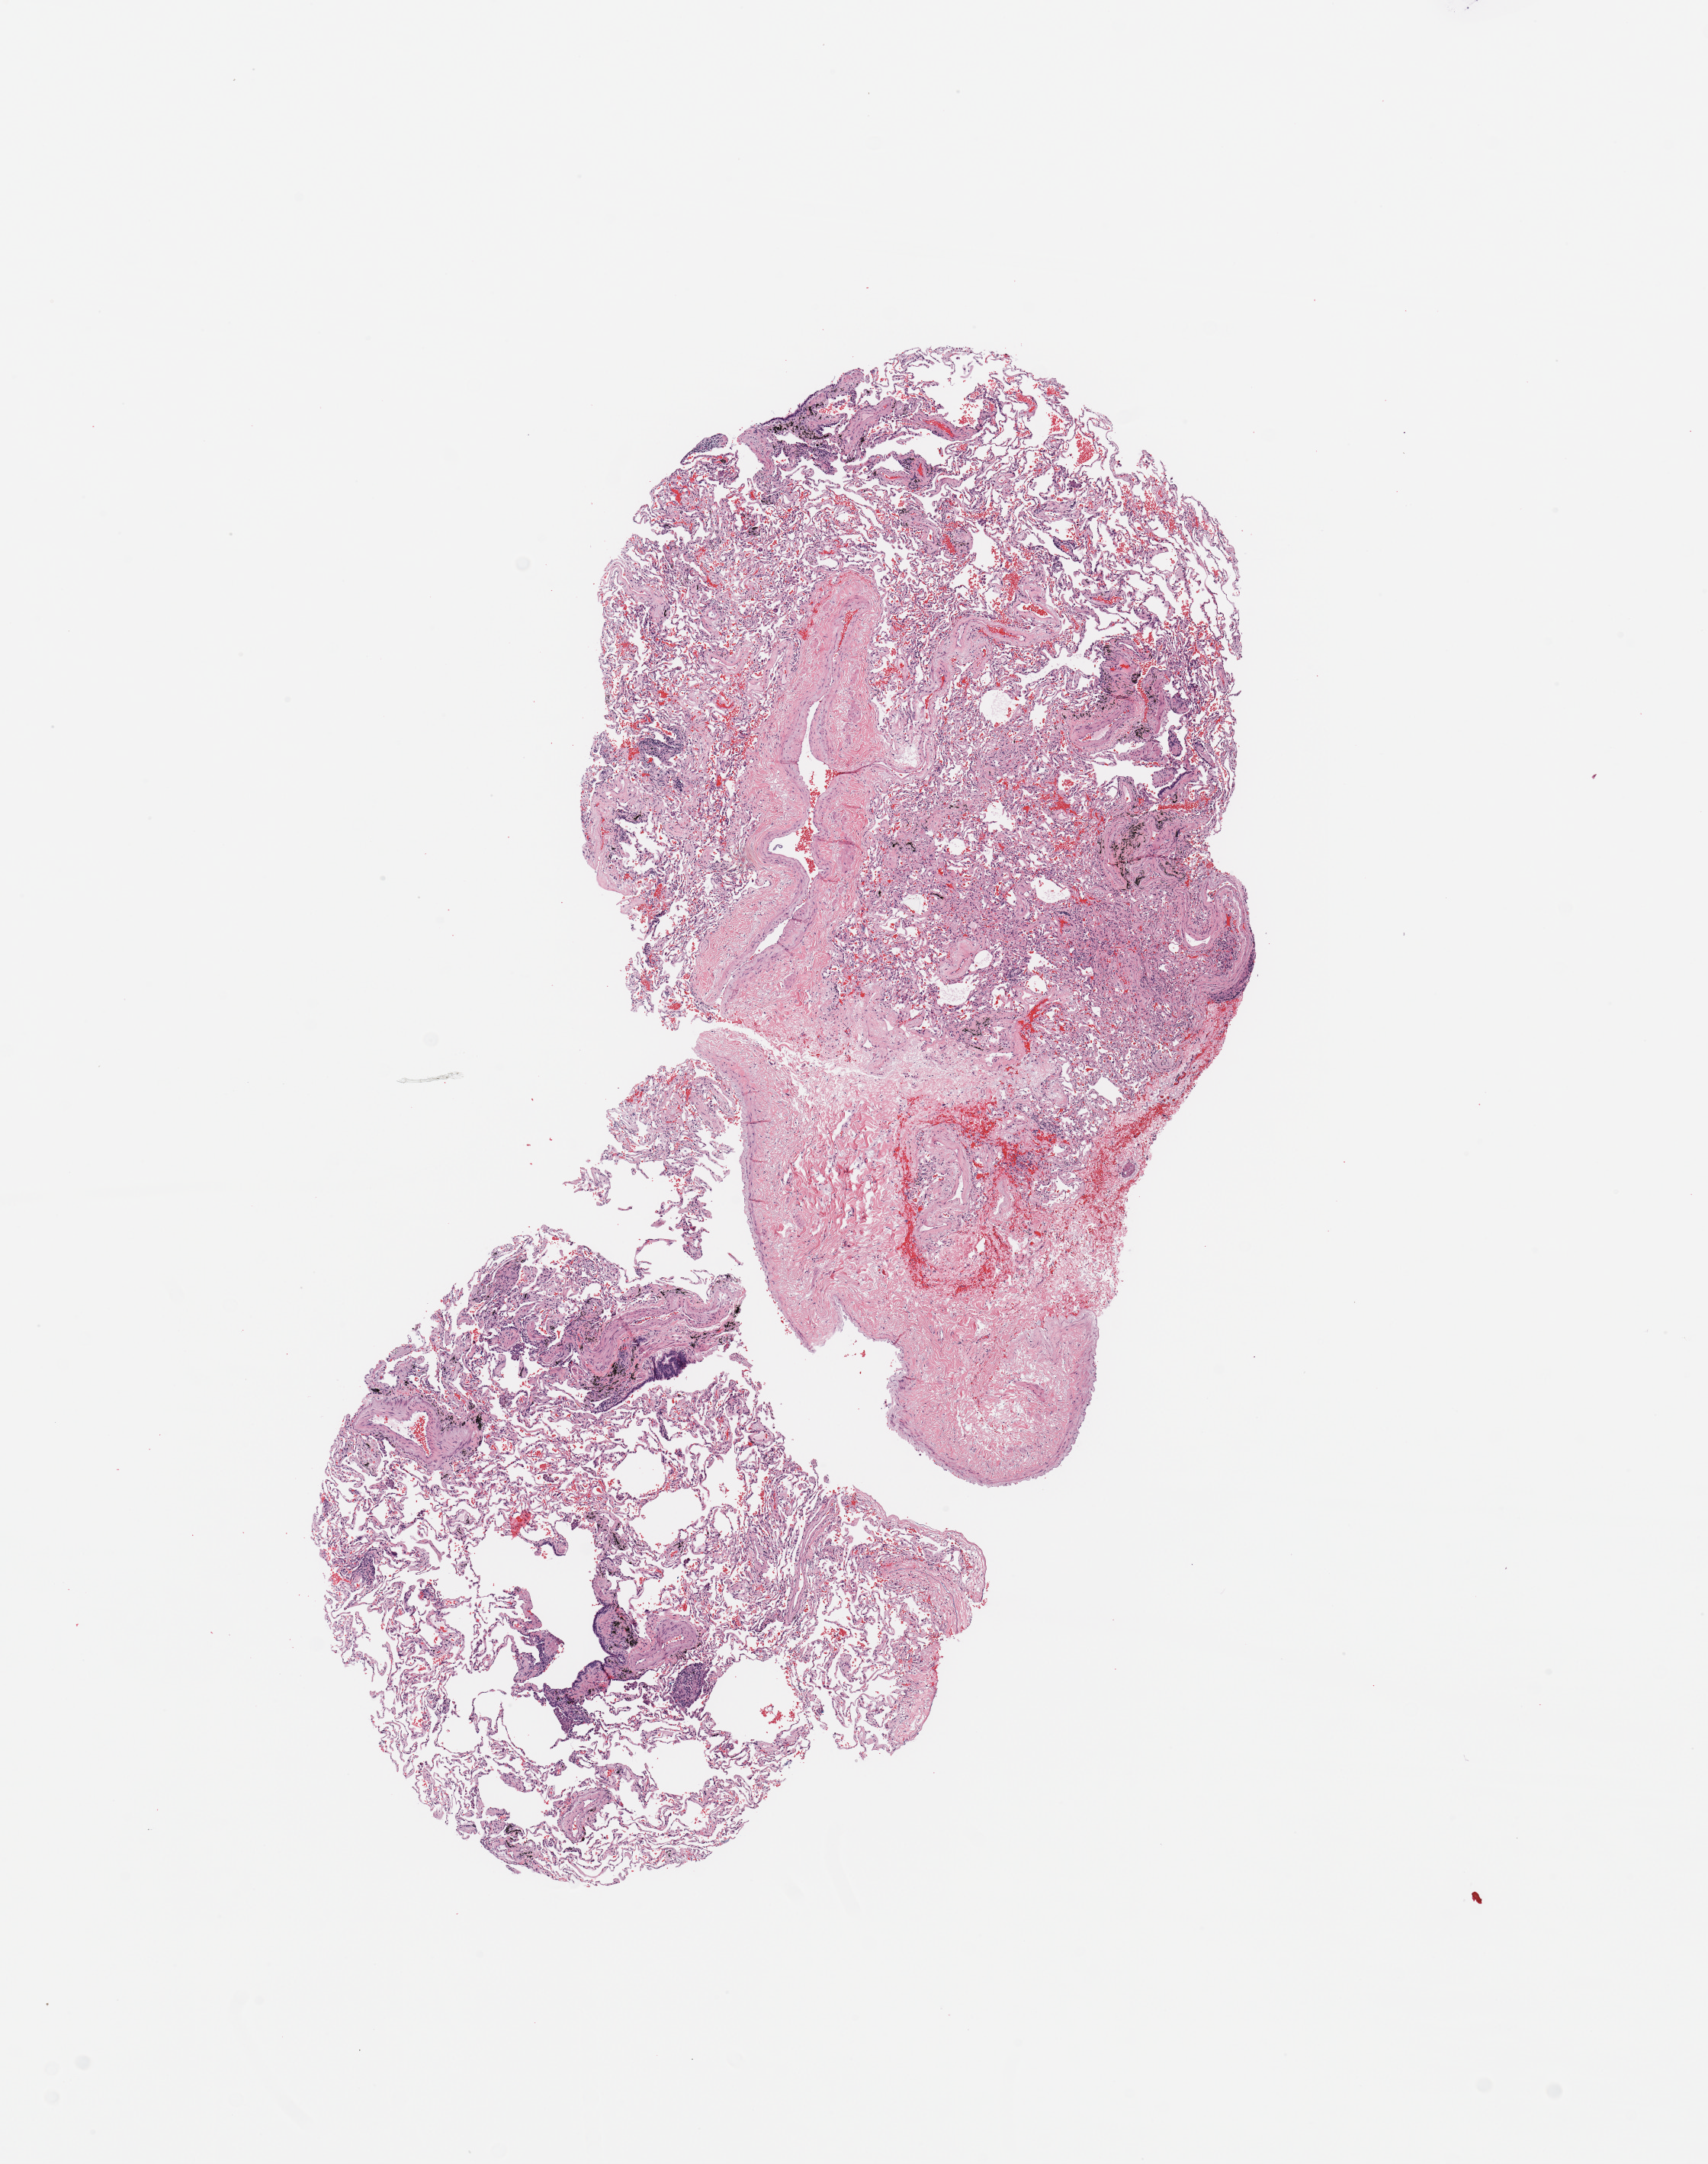
Digitized H&E tissue section (whole slide) — low-resolution overview of the scanned area, about 8.9 x 11.2 mm; normal (non-tumour) tissue sample, sampled site: lung. Female, 78 y/o.
• this section: normal (non-tumour) tissue from the same patient
• patient diagnosis: Adenocarcinoma, NOS